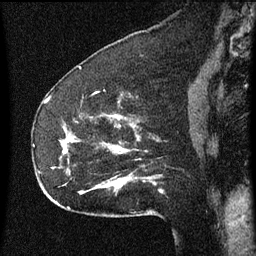
Breast MRI (dynamic contrast-enhanced), one sagittal slice; slice 22 of 60 in the series (ordered by position); dynamic contrast-enhanced series, image 2 of 3 at this slice position (ordered by acquisition); 1.5 T; TE 4.2 ms, TR 8 ms; 2 mm slice thickness; 256 × 256 image matrix. Female patient, age 52 years.
Structures marked on this image (semi-automatically segmented with operator editing):
- analysis volume of interest (the breast-tissue region the enhancement analysis was run in; not a lesion): bounding box <54,114,155,207> (left, top, right, bottom; pixels)
- tumour enhancement mask (voxels above the 70 % enhancement threshold inside the analysis volume of interest): <61,126,132,153>